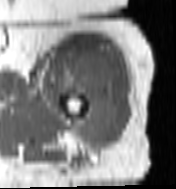
MRI of an extremity soft-tissue mass, one axial slice. Slice 85 of 100 in the series (ordered by position). MR volume resampled by the dataset authors to the PET/CT grid (not the native acquisition matrix). 3.27 mm slice thickness. 176 × 189 image matrix, field of view 172 × 185 mm. Female patient. Case-level facts recorded for this patient, not image findings: histological type: undifferentiated – high grade; grade: high; site of the primary tumour: left thigh.
Annotated regions visible in this slice (expert contour drawn on MRI and transferred to this co-registered scan by the dataset authors):
- gross tumour volume including surrounding oedema: bounding box <64,57,118,145> (left, top, right, bottom; pixels)
- gross tumour volume (mass): <66,57,118,143>